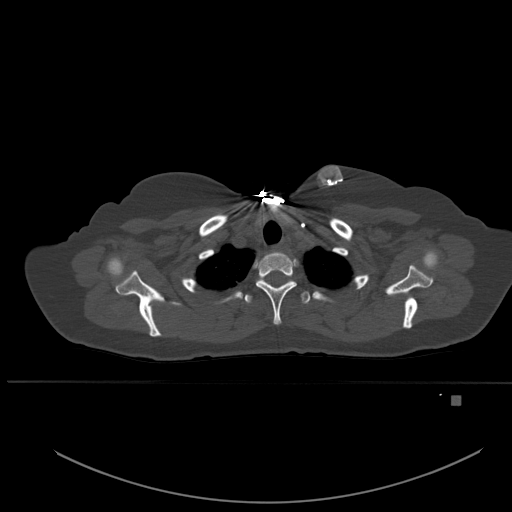
CT including the spine, one axial slice. Bone window (W 1800 / L 400 HU). 1.5 mm slice thickness. 512 × 512 image matrix, field of view 443 × 443 mm. Patient: female, 49 years. From the clinical record (not read from this slice): primary cancer: breast.
Structures marked on this image (semi-automatic segmentation, software-assisted and operator-edited):
- T1 vertebra: bounding box (x1, y1, x2, y2) in pixels: (256, 251, 297, 325)
- T2 vertebra: (244, 279, 311, 304)